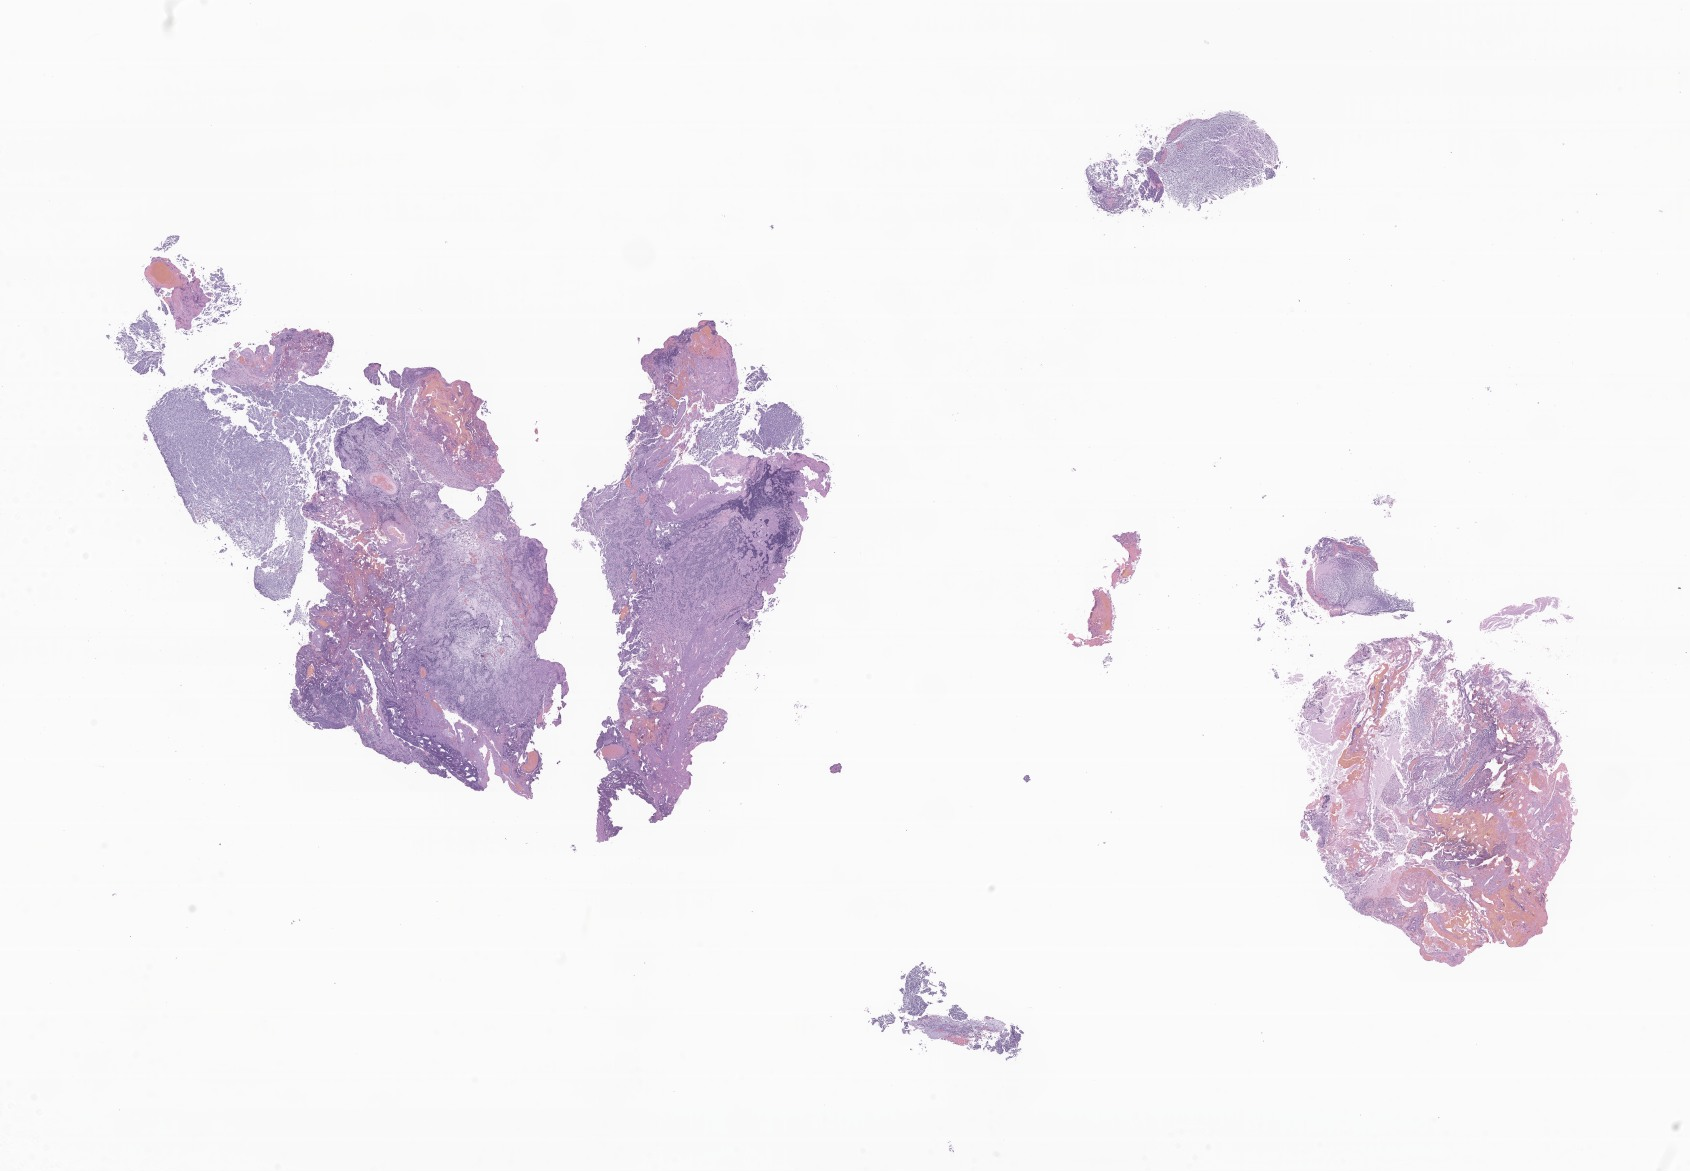
Digitized H&E-stained section of tumor tissue from the brain — low-resolution overview of the scanned area, about 28.5 x 19.8 mm, formalin-fixed, paraffin-embedded (FFPE) tissue. Patient: male, age 101 months (8 years 5 months).
Diagnosis (ICD-O-3 morphology term): Medulloblastoma, NOS.